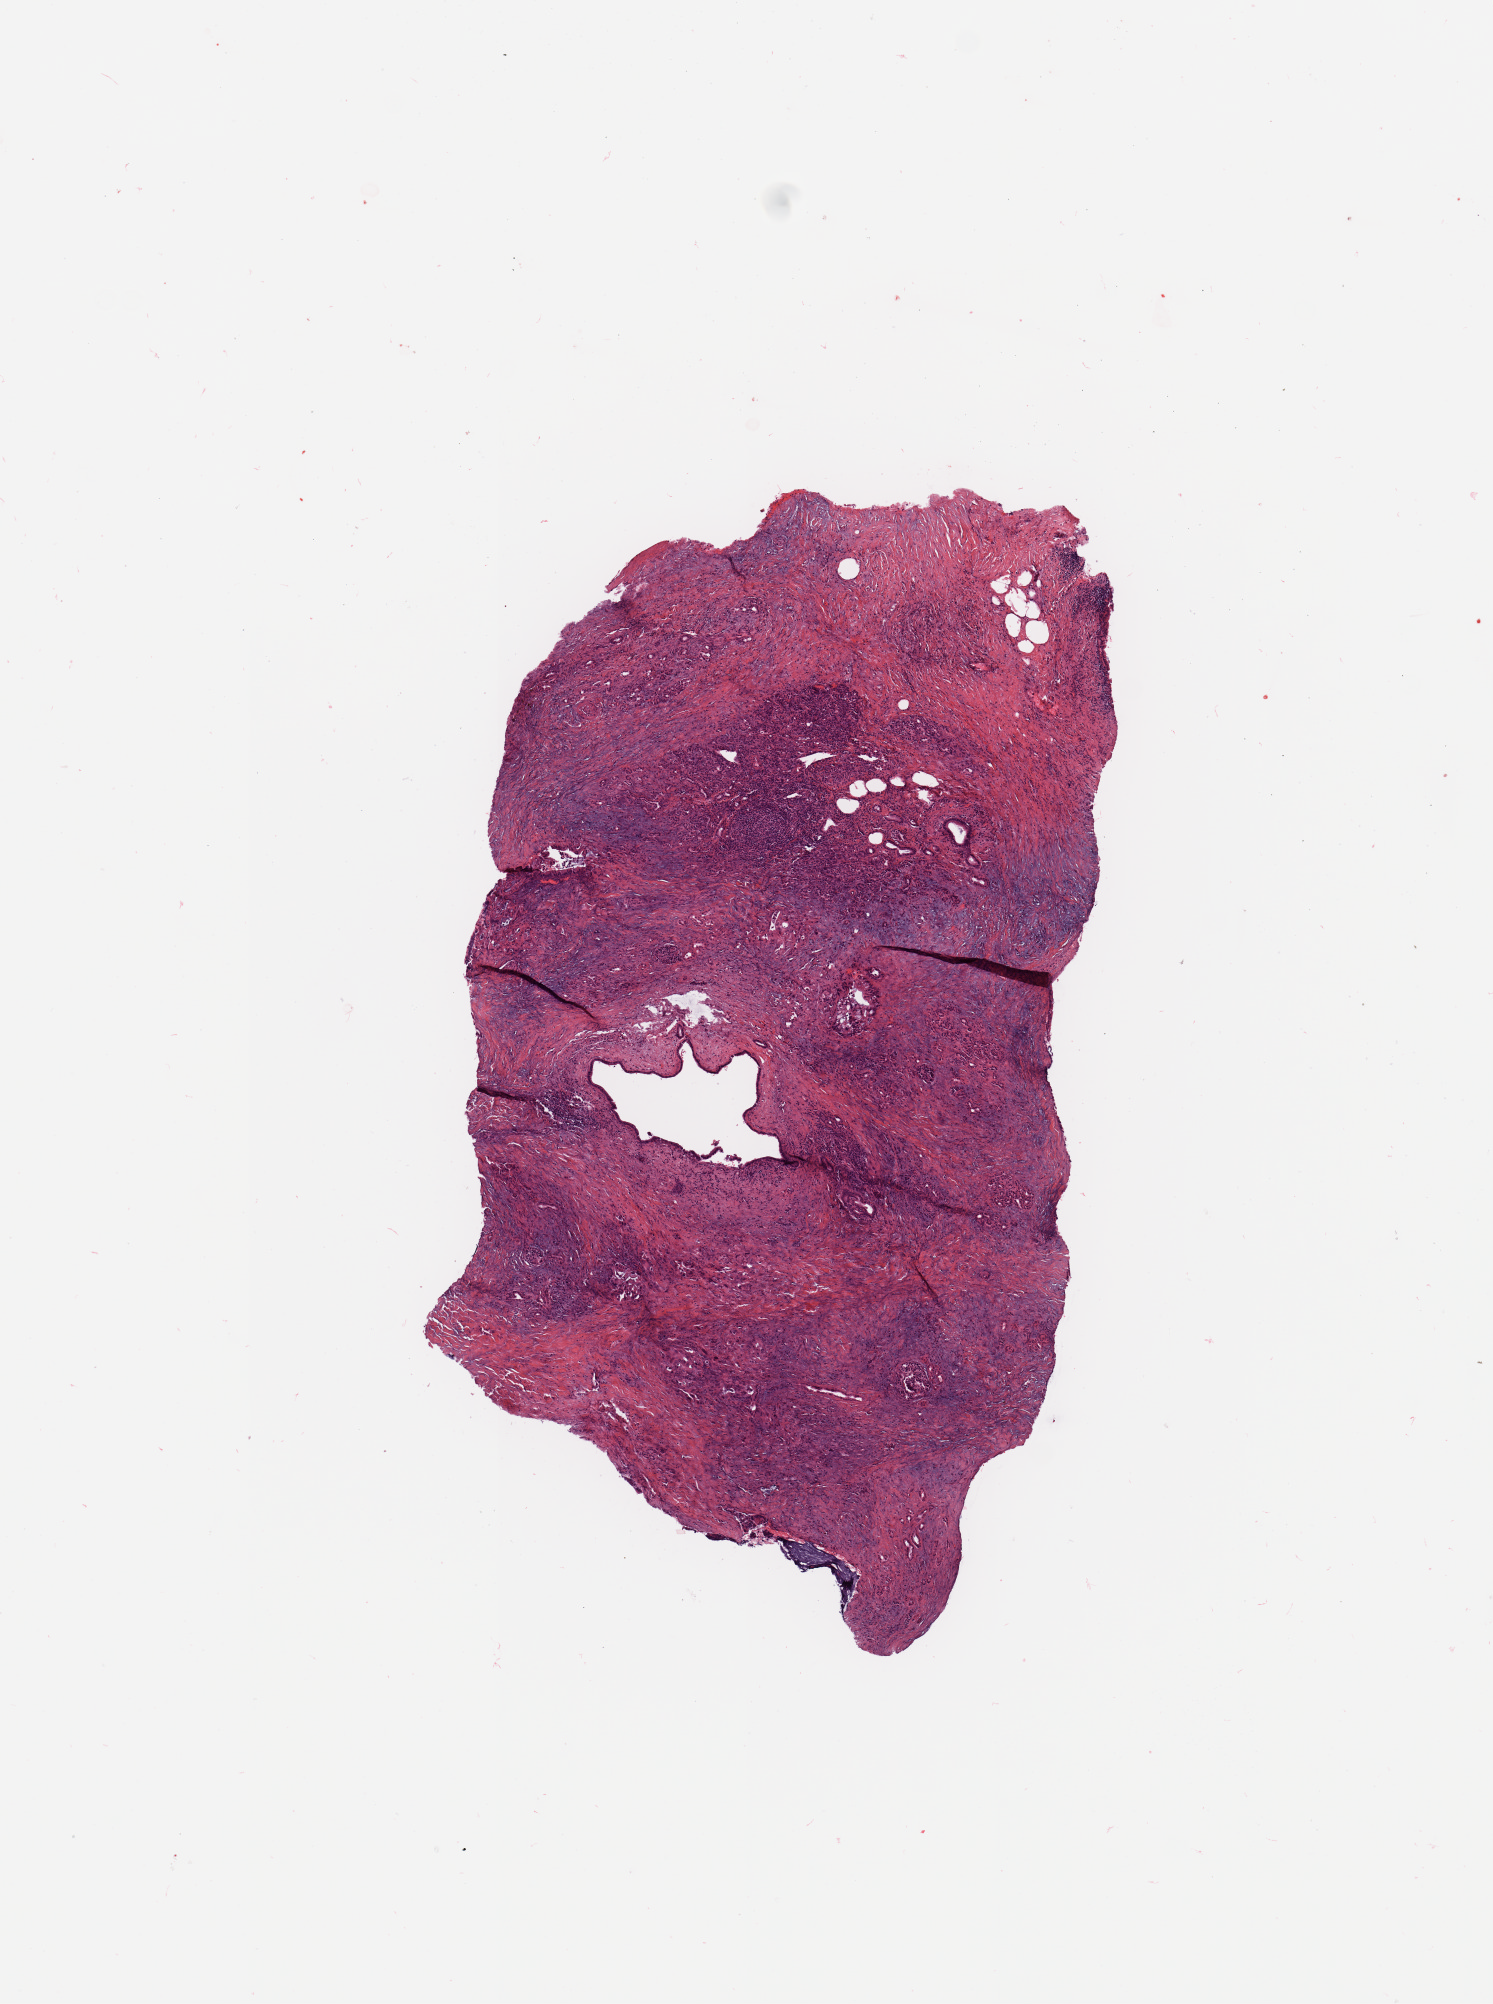
Hematoxylin and eosin (H&E) stained whole-slide image — shown as a low-resolution overview of the whole scanned area (about 5.9 x 7.9 mm, slide scanned at 20x), tumour tissue sample, sampled site: pancreas. Male, 66 y/o. Histologic grade: G3 (poorly differentiated). Composition of this section per pathologist review: tumour nuclei 10%, necrosis 0%.
AJCC pathologic stage: IIA. Primary tumour site (as recorded): head. Diagnosis: Infiltrating duct carcinoma, NOS.